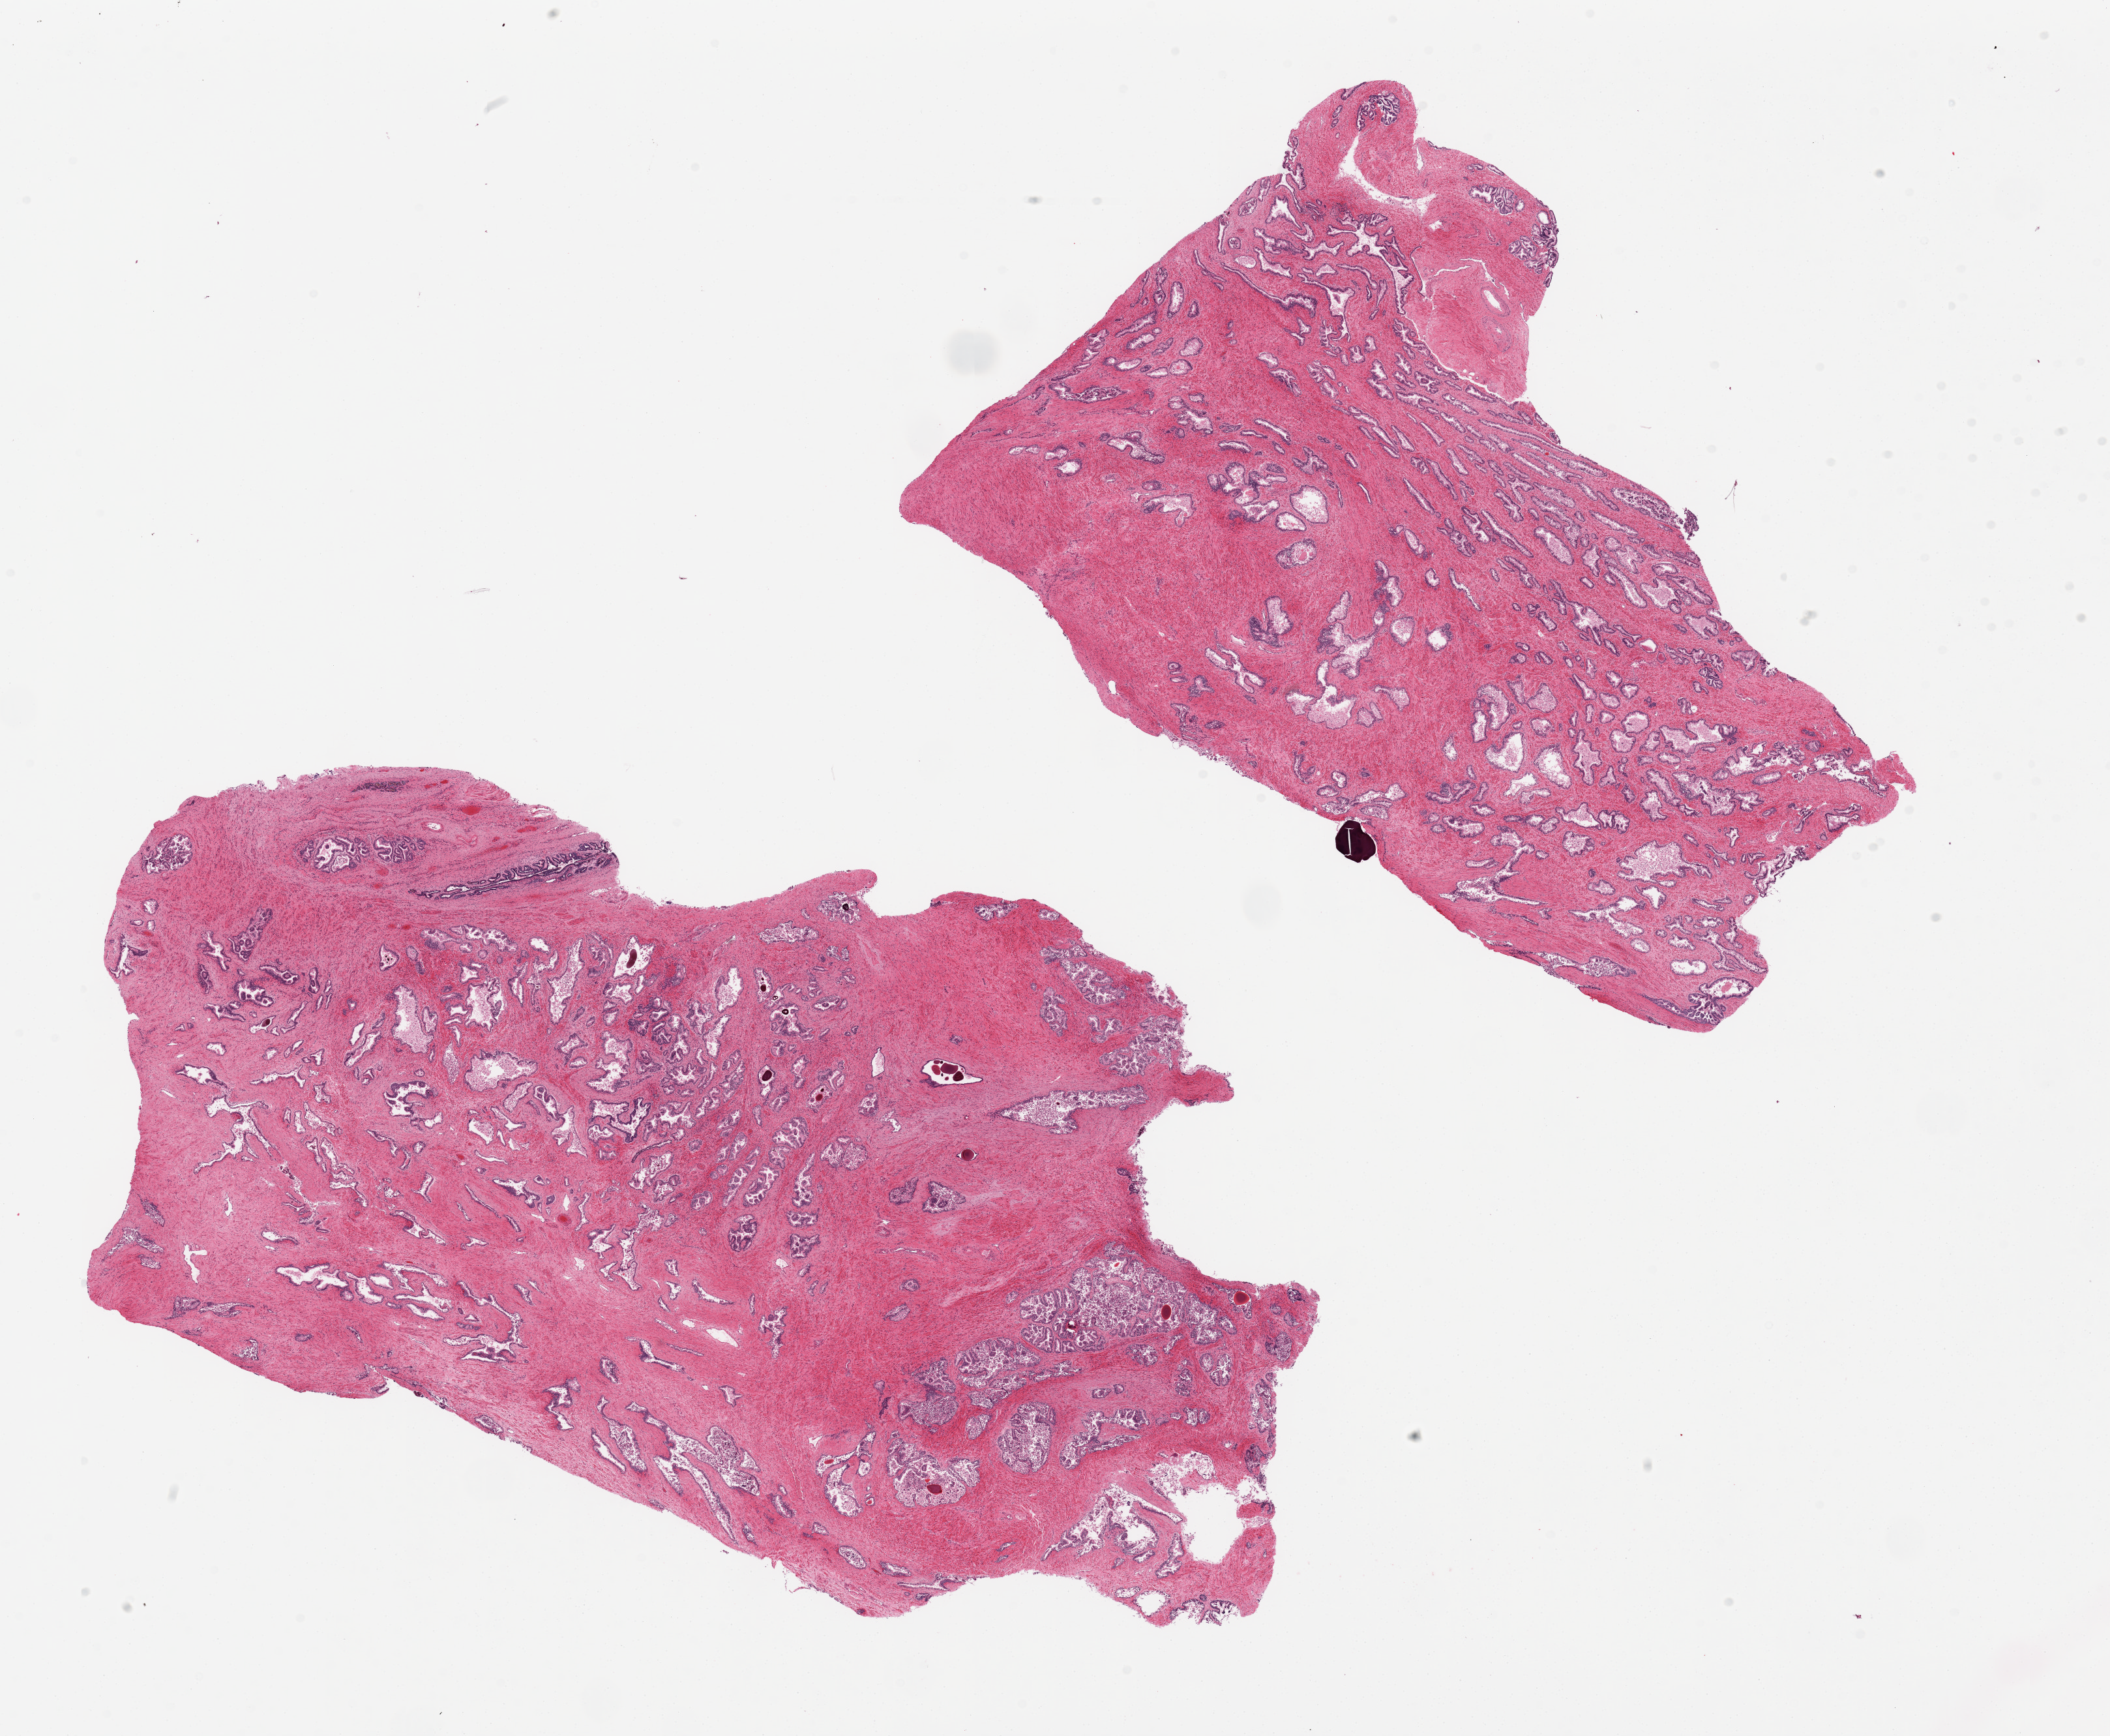
Whole-slide image, haematoxylin and eosin stain, whole scanned area (about 25.6 x 21.1 mm) shown as a low-resolution overview, PAXgene-fixed paraffin-embedded (PFPE) section, section of prostate (target tissue), tissue donor sample. Male donor.
Reviewer comment on this tissue sample: 2 pieces.